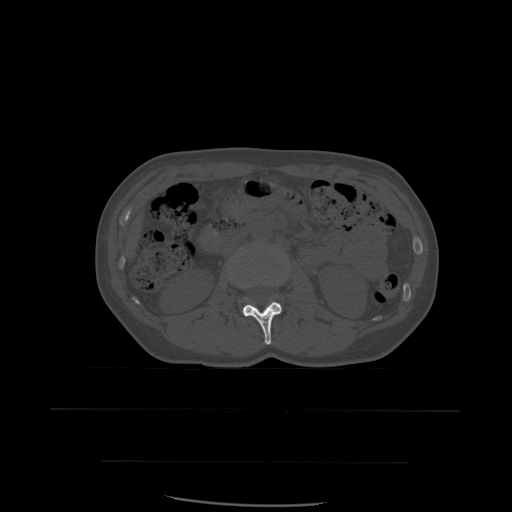
CT including the spine, one axial slice; position 215 of 574 along the scan axis; bone window (W 1800 / L 400 HU); 1.25 mm slice thickness; 512 × 512 image matrix, field of view 392 × 392 mm. Patient age 48 years. Case-level facts recorded for this patient, not image findings: primary cancer: lung.
Annotated regions visible in this slice (semi-automatic segmentation, software-assisted and operator-edited):
- L2 vertebra: bounding box <243,302,282,346> (left, top, right, bottom; pixels)